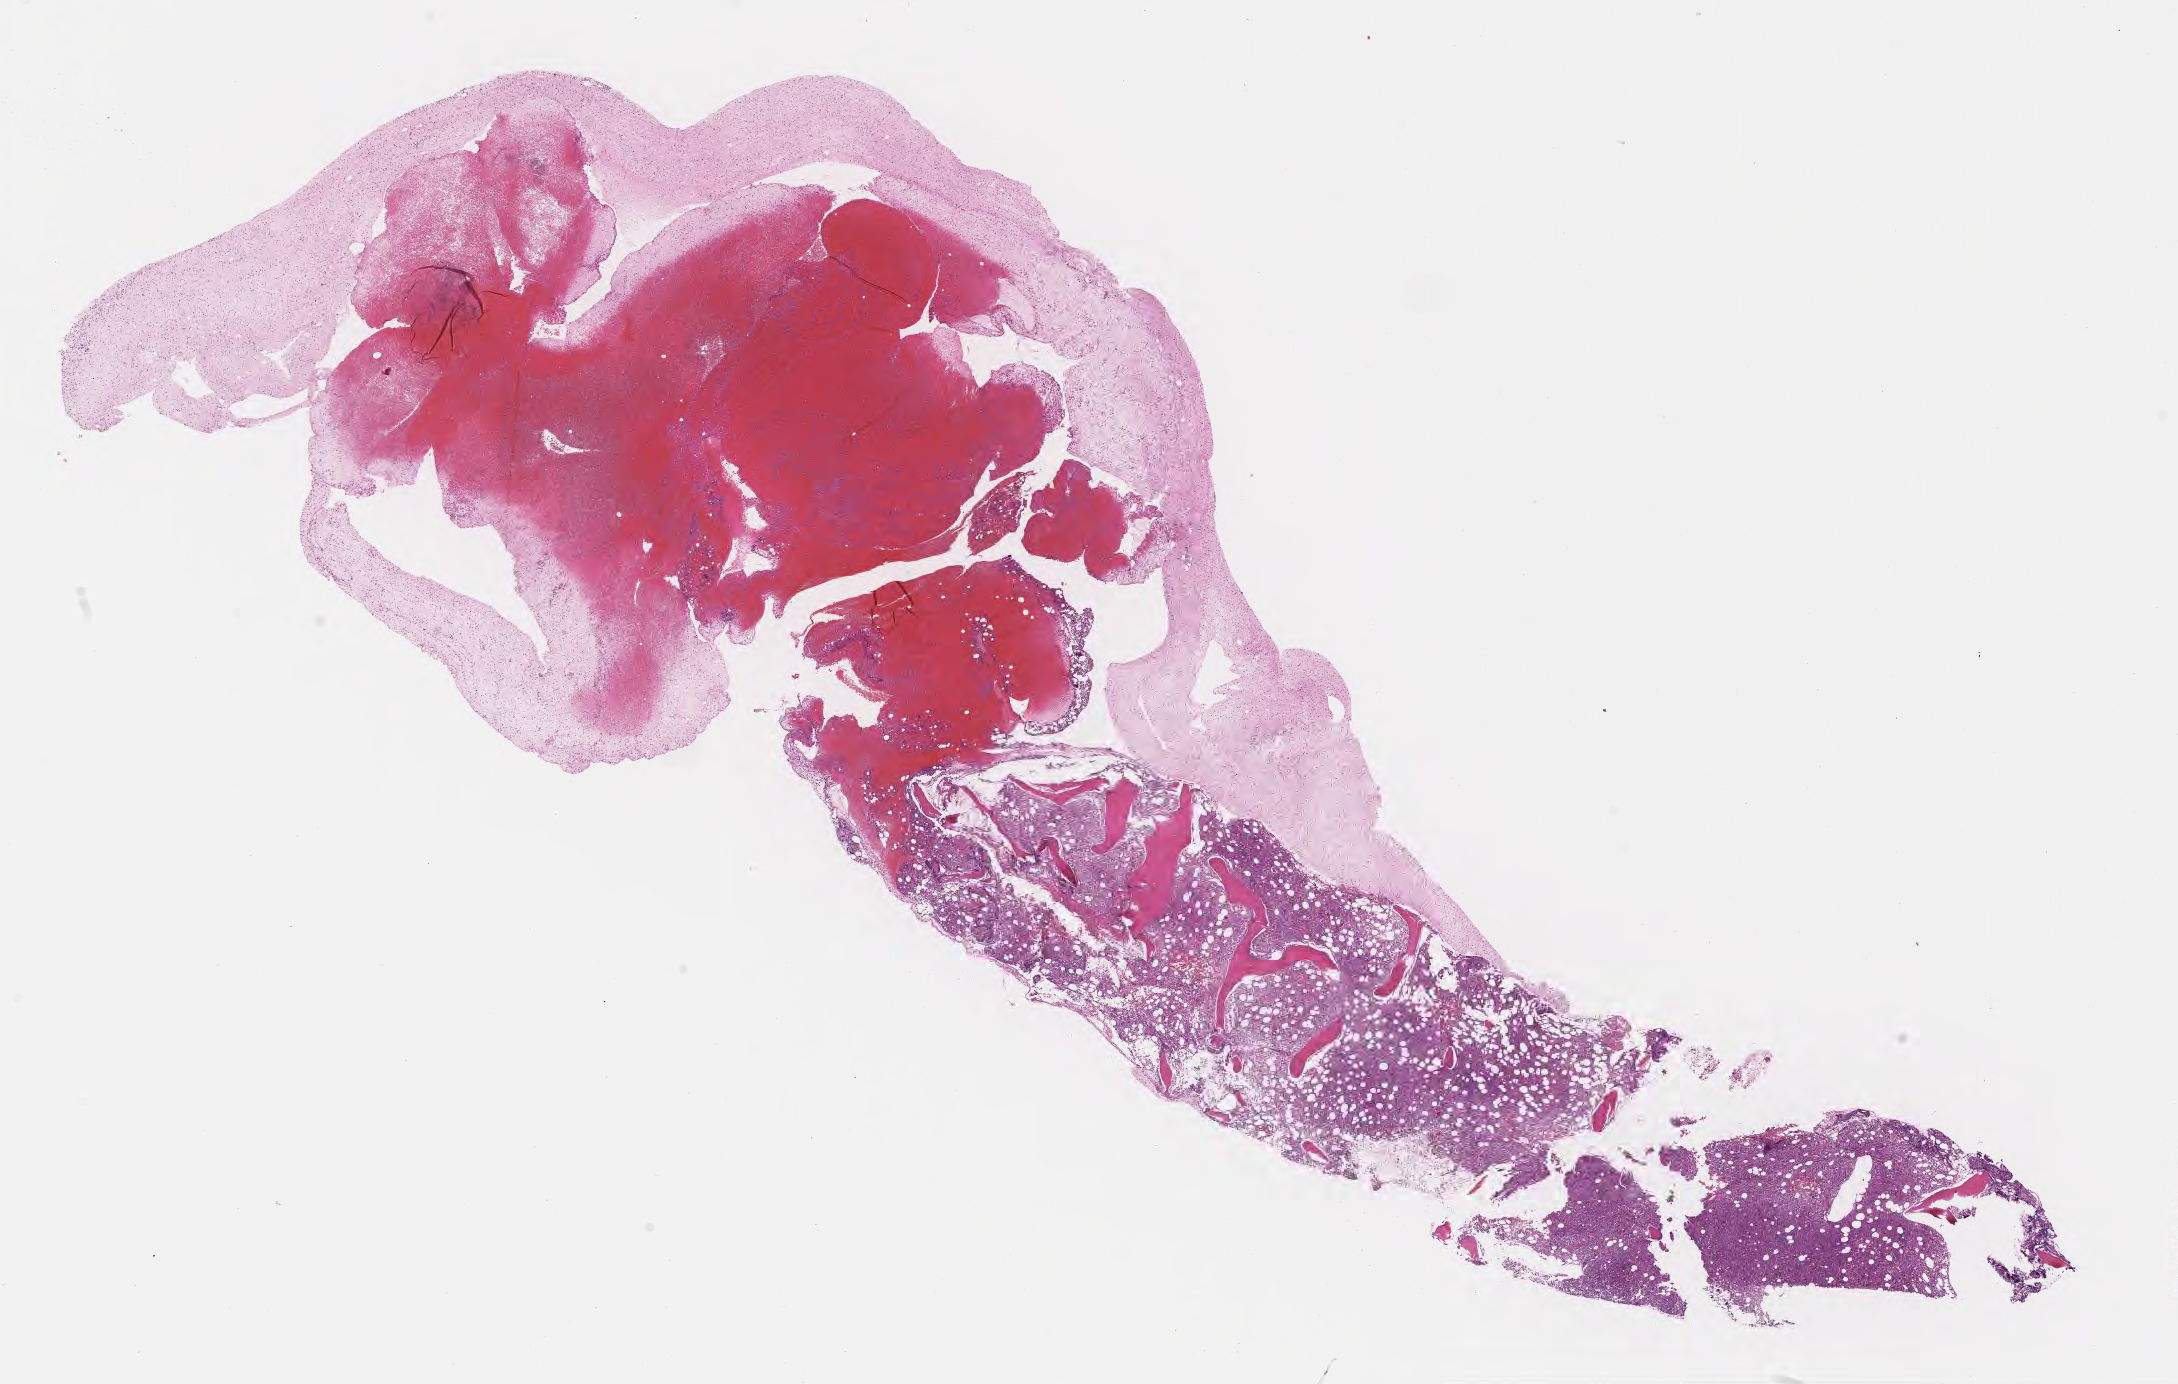
Whole-slide image, haematoxylin and eosin stain, a low-resolution overview of the entire scanned area, about 17.6 x 11.2 mm. Formalin-fixed paraffin-embedded section. Specimen: normal-tissue sample (non-tumor) from a patient with burkitt lymphoma, NOS. Female patient, age 45 years. Composition of this section per pathologist review: tumor cells 0%, tumor nuclei 0%.
This section: non-tumor tissue sample; the patient's diagnosis is given above. Section: top of the tissue portion.